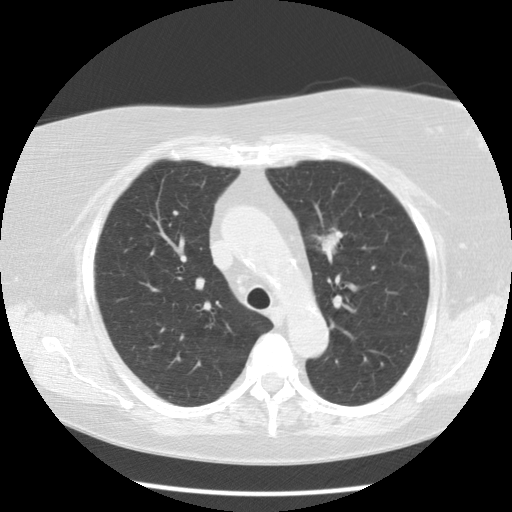
Low-dose screening chest CT, one axial slice; slice 82 of 109 in the series (ordered by position); lung window (W 1500 / L -600 HU); 2.5 mm slice thickness; 512 × 512 image matrix, field of view 334 × 334 mm.
Structures marked on this image (expert manual segmentation):
- lesion 1 (tumor, upper lobe of left lung): bounding box [x1, y1, x2, y2] px = [315, 229, 343, 261]